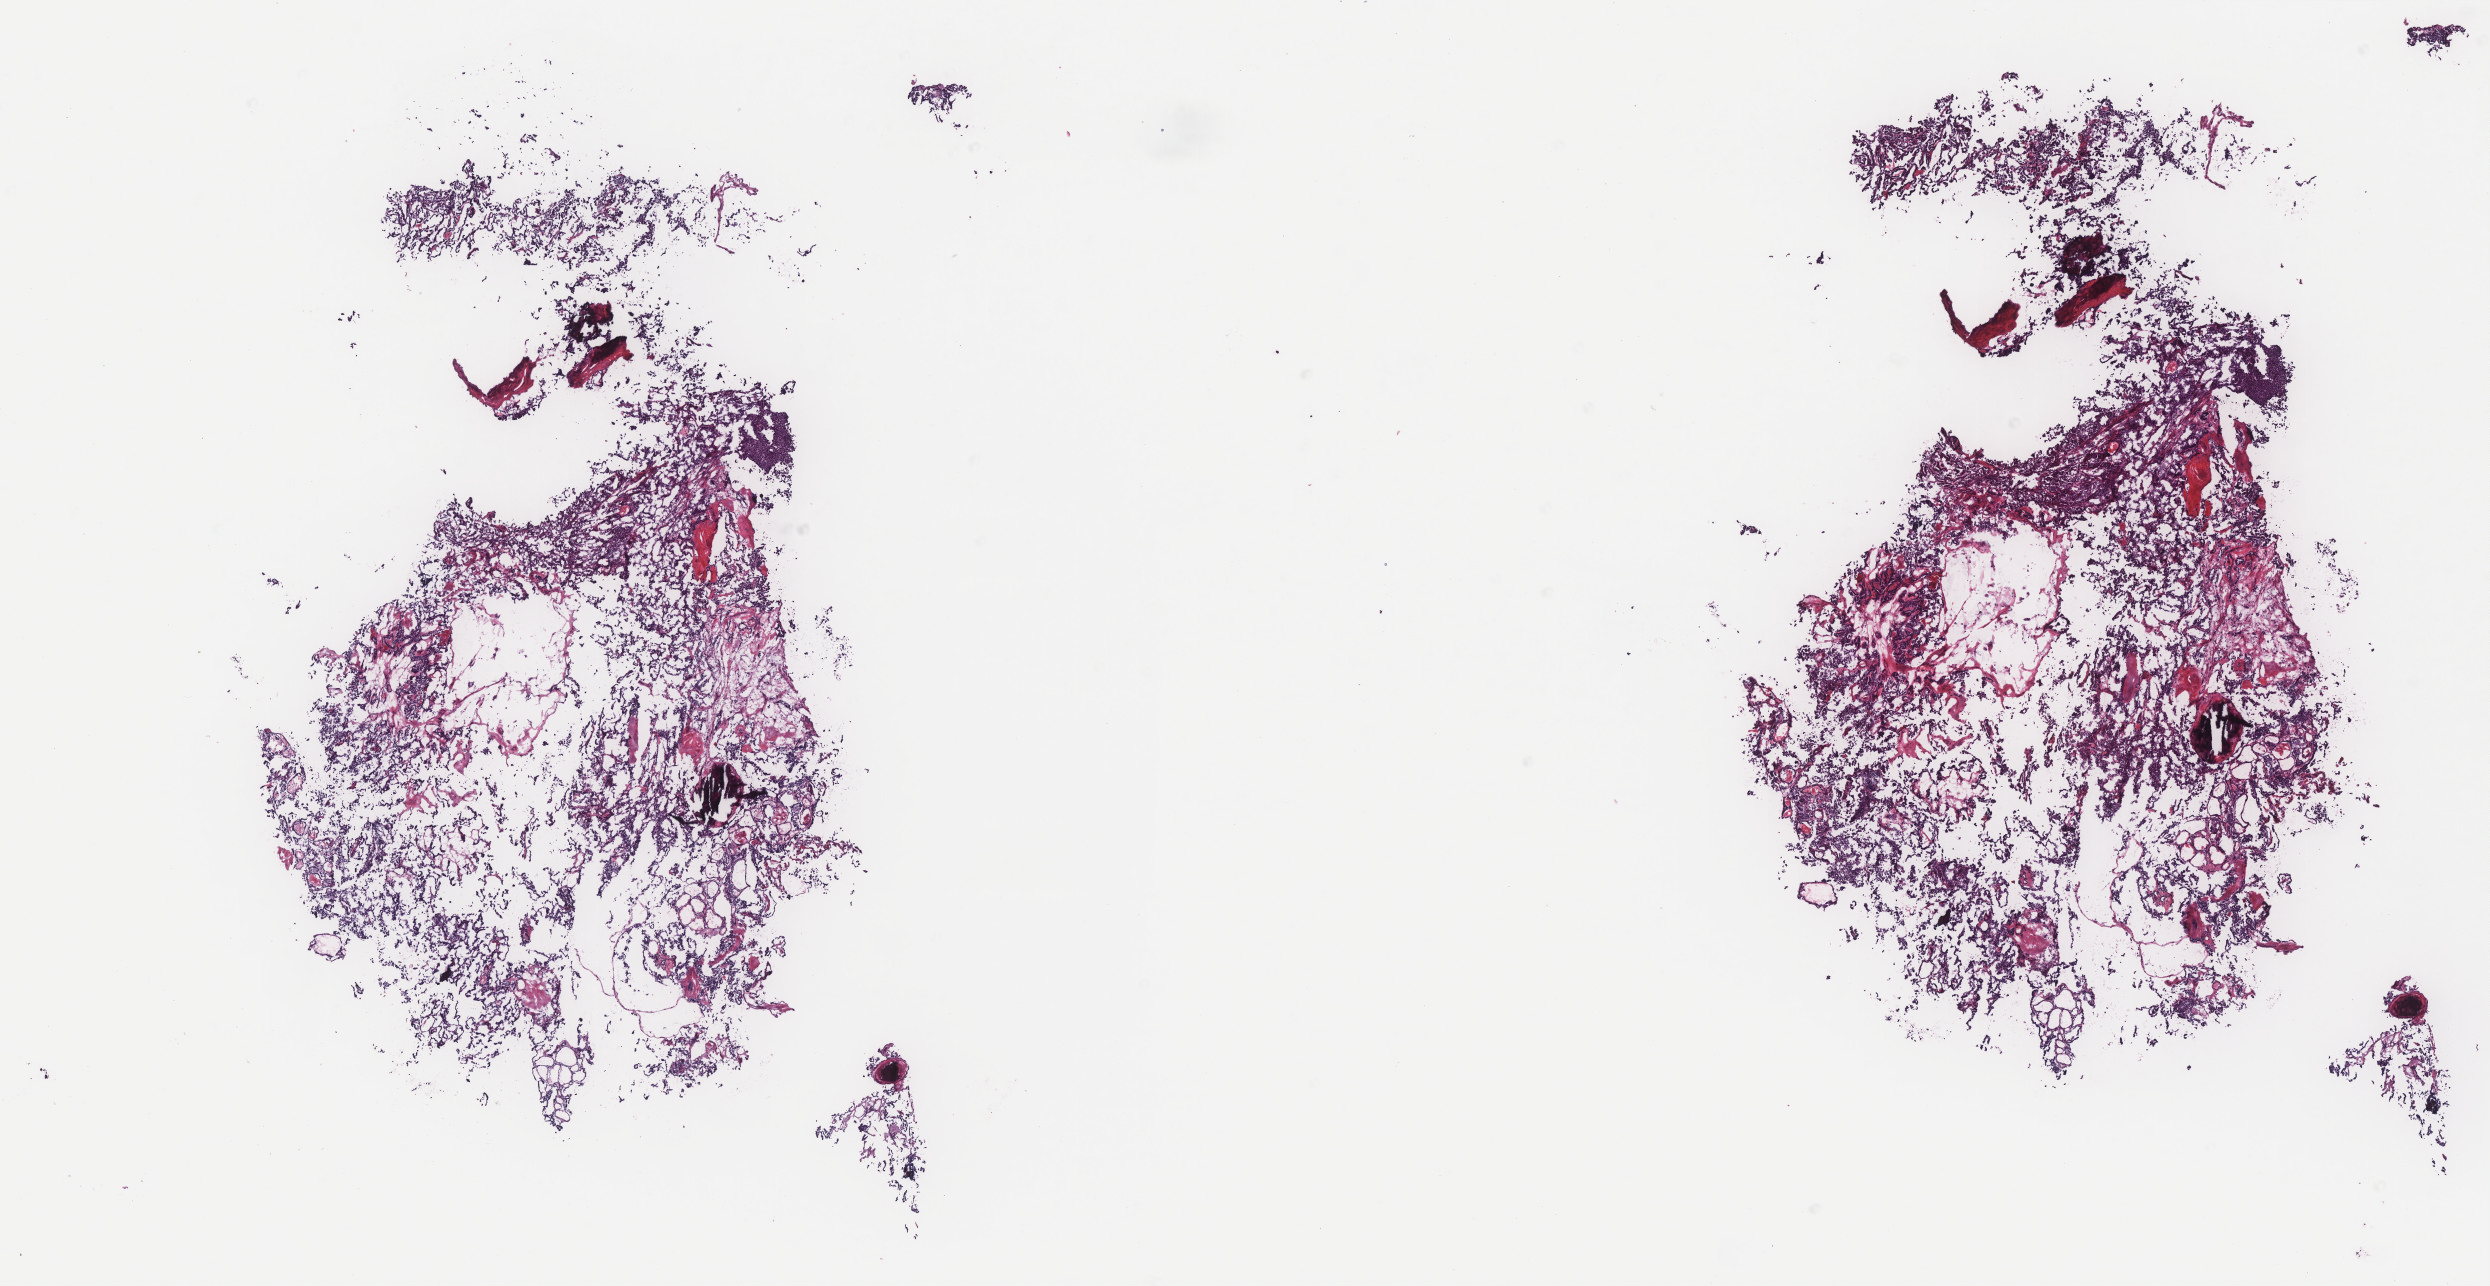
Whole-slide histology image, H&E — low-resolution overview of the scanned area, about 20.0 x 10.3 mm (acquisition: 40x scan); frozen section from the top of the tissue portion; primary tumour sample from the thyroid. Patient: female, age at initial diagnosis 52 years. Pathologist review of this section (percent, as recorded): tumour cells 95%, tumour nuclei 99%, normal cells 0%, stromal cells 5%, necrosis 0%. Infiltration values recorded for this section: lymphocyte infiltration 1%, monocyte infiltration 0%, neutrophil infiltration 0%.
- TNM: T2 N1b MX
- laterality: bilateral
- AJCC pathologic stage: IVA (7th edition)
- lymph nodes positive (case pathology): 1 of 4 examined
- pathologic diagnosis: Papillary carcinoma, columnar cell (thyroid gland)